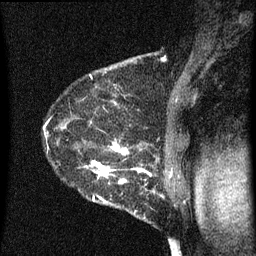
Breast MRI (dynamic contrast-enhanced), one sagittal slice. Position 50 of 60 along the scan axis. Dynamic contrast-enhanced series, image 2 of 3 at this slice position (ordered by acquisition). 1.5 T. TE 4.2 ms, TR 8 ms. 2 mm slice thickness. 256 × 256 image matrix, field of view 180 × 180 mm. Female patient, age 54 years.
Structures marked on this image (semi-automatically segmented with operator editing):
- analysis volume of interest (the breast-tissue region the enhancement analysis was run in; not a lesion): bounding box [x1, y1, x2, y2] px = [49, 138, 164, 209]
- tumour enhancement mask (voxels above the 70 % enhancement threshold inside the analysis volume of interest): [49, 138, 156, 203]